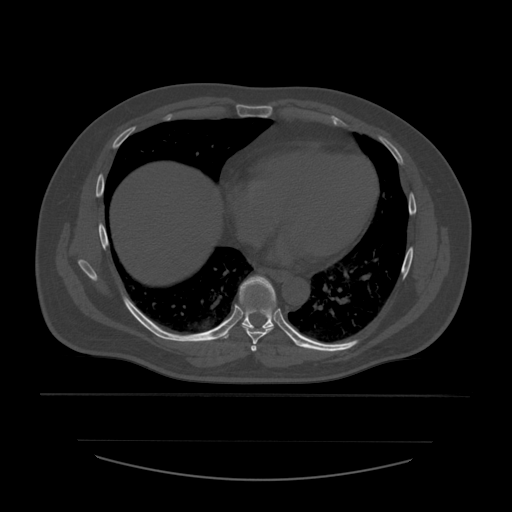
CT including the spine, one axial slice; 120 kVp; bone window (W 1800 / L 400 HU); 1.25 mm slice thickness; 512 × 512 image matrix, field of view 441 × 441 mm. Patient age 44 years. Case-level facts recorded for this patient, not image findings: primary cancer: soft tissue sarcoma.
Structures marked on this image (semi-automatic segmentation, software-assisted and operator-edited):
- T6 vertebra: bounding box (x1, y1, x2, y2) in pixels: (251, 344, 257, 353)
- T7 vertebra: (242, 312, 274, 345)
- T8 vertebra: (223, 276, 277, 339)